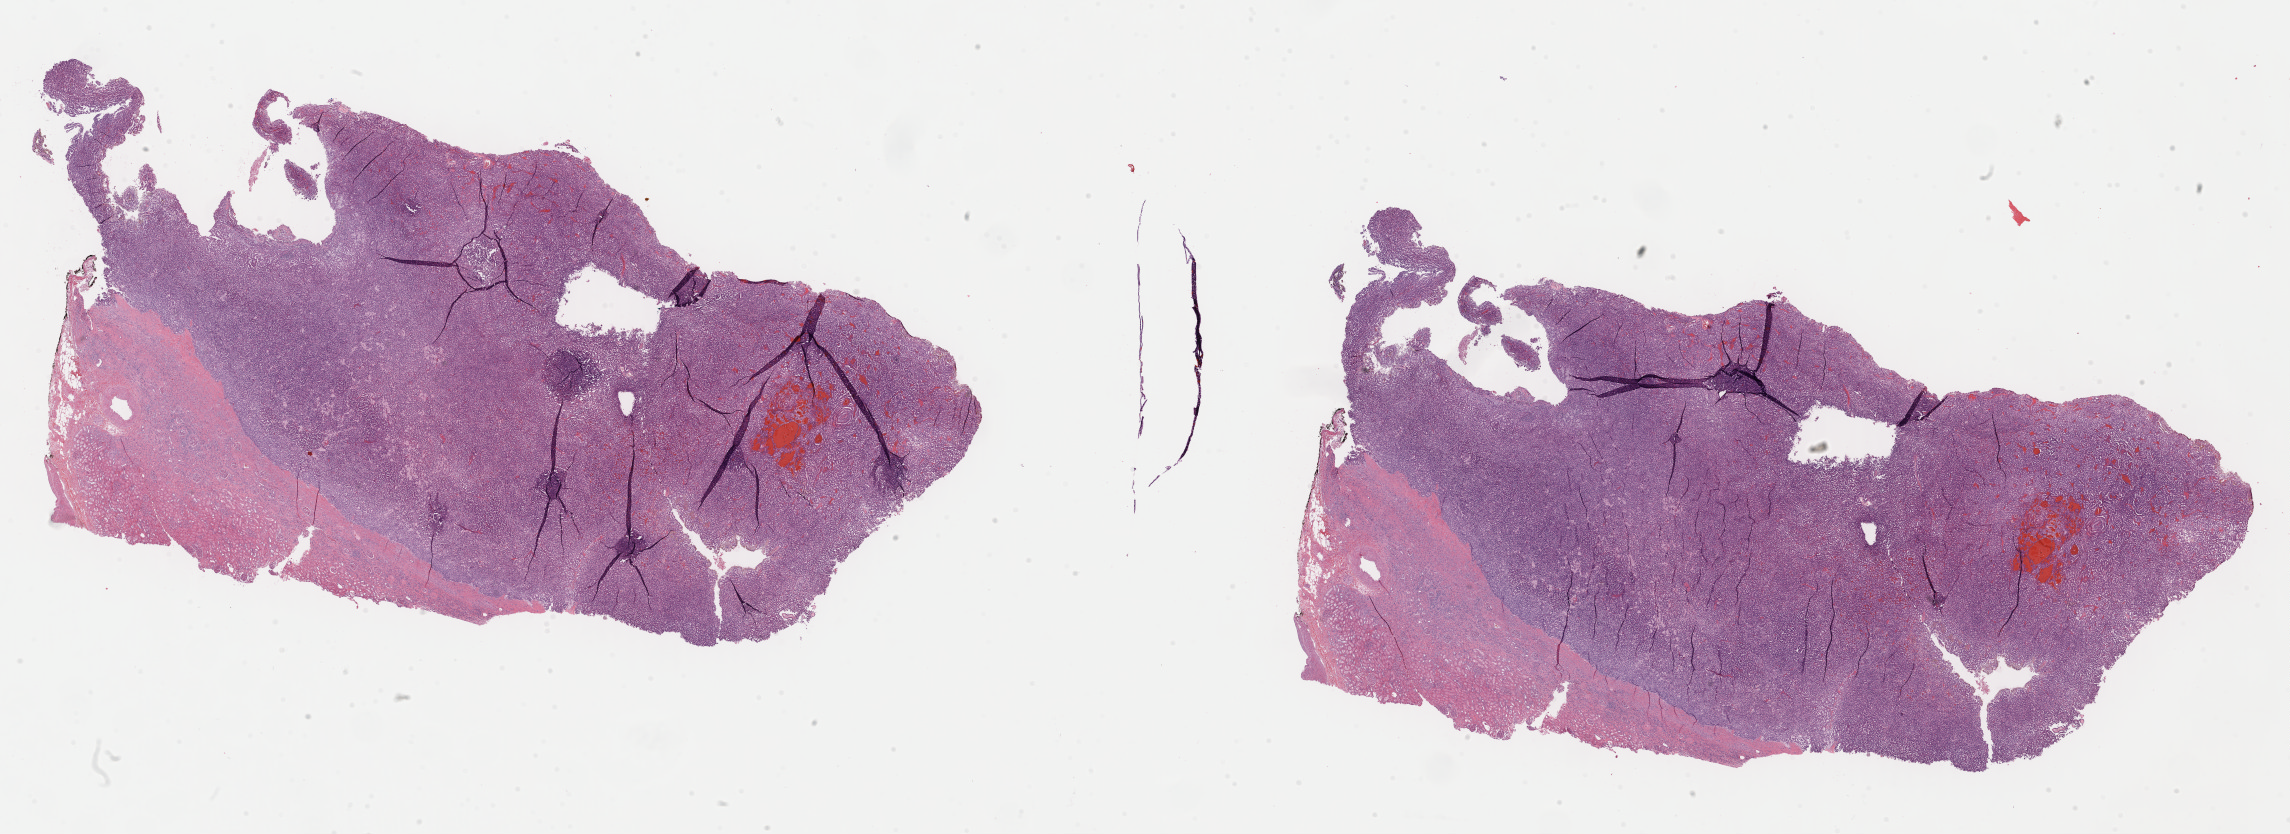
Whole-slide histology image, H&E-stained — shown as a low-resolution overview of the whole scanned area (about 36.1 x 13.2 mm, acquisition: 40x scan); FFPE section; kidney, primary tumour sample. Male patient; age at initial diagnosis 51 years.
AJCC pathologic stage: I (7th edition). Diagnosis: Papillary adenocarcinoma, NOS.